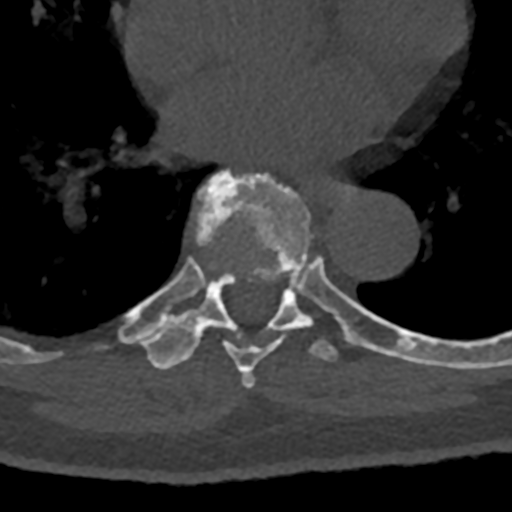
CT including the spine, one axial slice; position 735 of 797 along the scan axis; reconstruction kernel Br40s/3; 120 kVp; bone window (W 1800 / L 400 HU); 512 × 512 image matrix. Patient: male, 74 years. Case-level facts recorded for this patient, not image findings: primary cancer: renal; vertebrae with lytic lesions (as recorded): T10, L1, L2, L3, L4, L5.
Outlined on this slice (semi-automatic segmentation, software-assisted and operator-edited):
- T7 vertebra: bounding box [x1, y1, x2, y2] px = [196, 169, 364, 389]
- T8 vertebra: [119, 273, 432, 370]